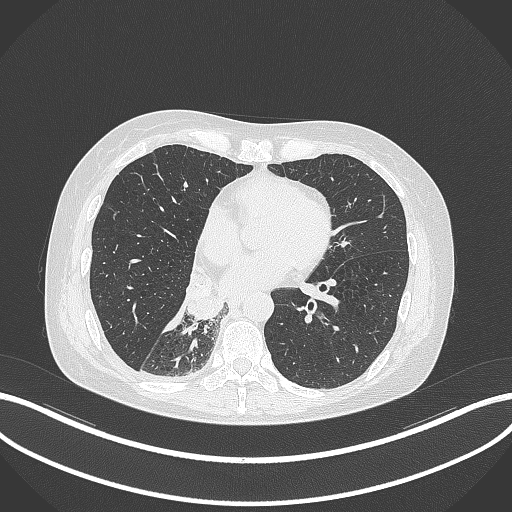
Chest CT, one axial slice; position 123 of 329 along the scan axis; reconstruction kernel B70f; 120 kVp; lung window (W 1500 / L -600 HU); 1 mm slice thickness; 512 × 512 image matrix, field of view 400 × 400 mm. Patient: female, 63 years. Case-level facts recorded for this patient, not image findings: clinical TNM (as recorded): T1c N0 M0.
Outlined on this slice (bounding box drawn by a radiologist):
- lung tumour (recorded histology: adenocarcinoma): bounding box (x1, y1, x2, y2) in pixels: (184, 271, 224, 320)